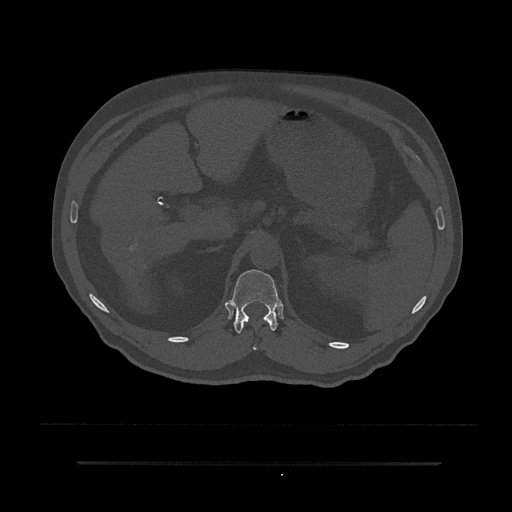
CT including the spine, one axial slice; position 220 of 797 along the scan axis; 120 kVp; bone window (W 1800 / L 400 HU); 0.5 mm slice thickness; 512 × 512 image matrix, field of view 464 × 464 mm. Male patient, age 59 years. From the clinical record (not read from this slice): primary cancer: bile ducts.
Outlined on this slice (semi-automatically segmented with operator editing):
- T12 vertebra: bounding box [x1, y1, x2, y2] px = [228, 269, 282, 350]